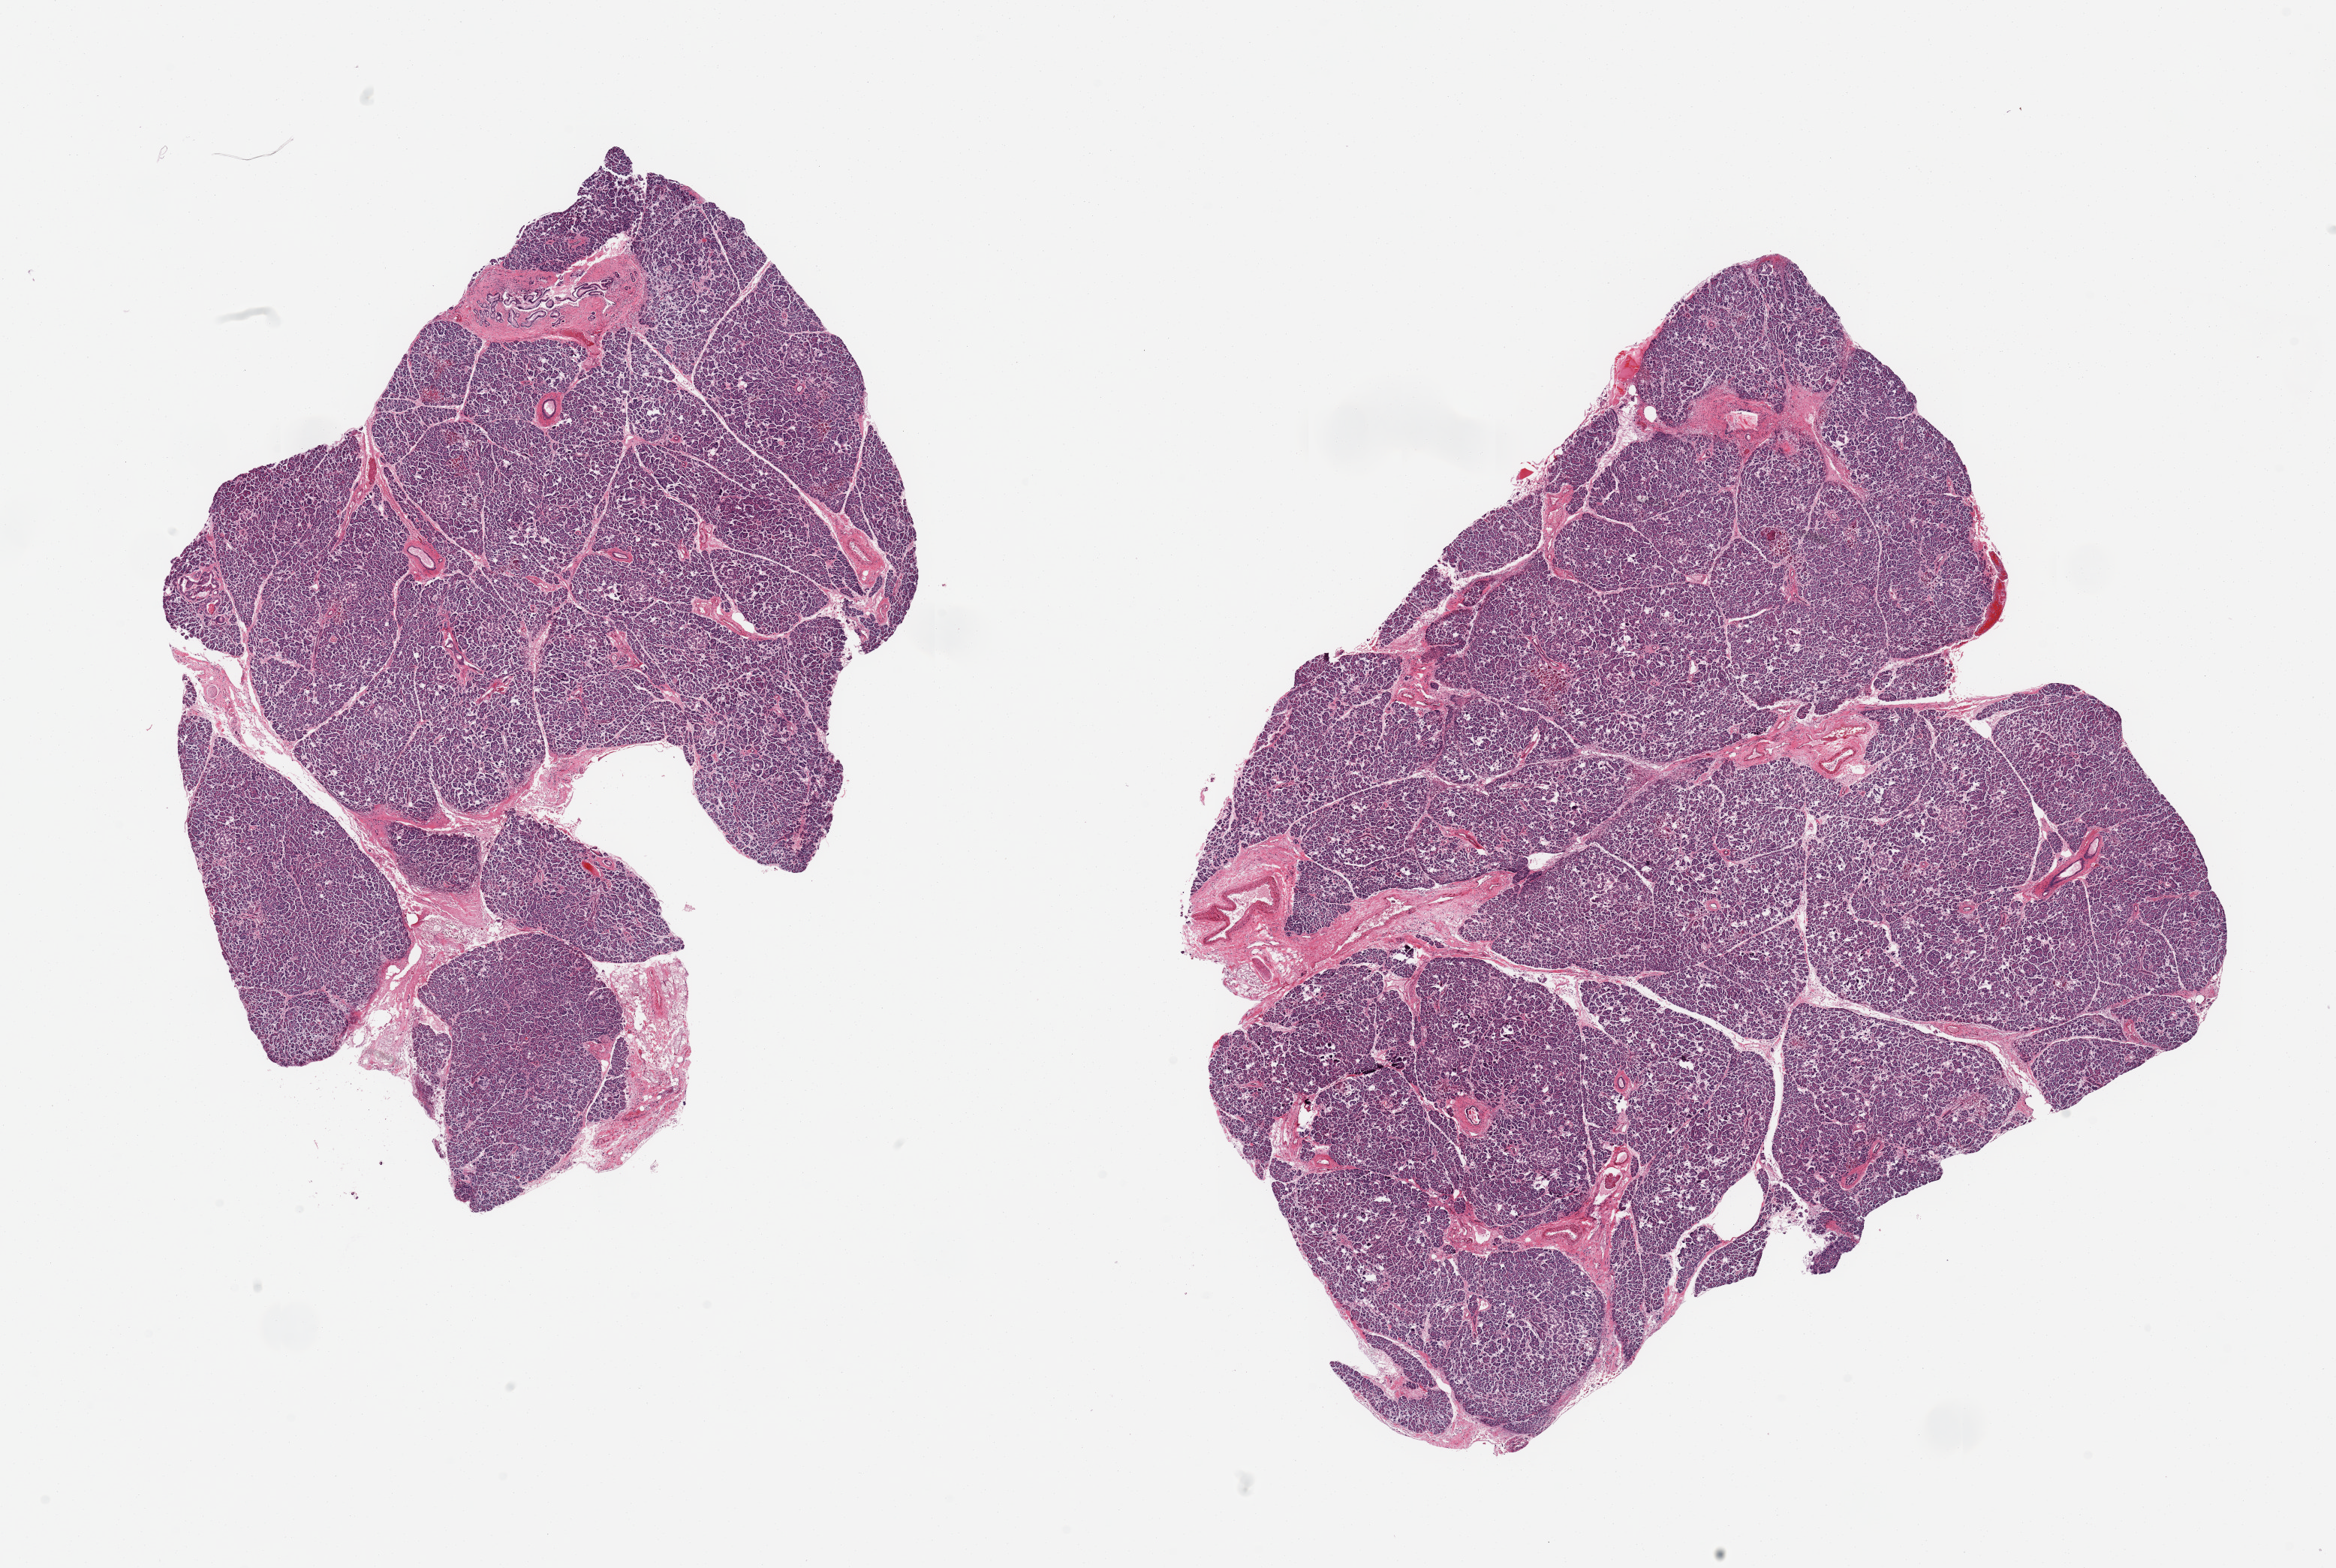
Whole-slide image, hematoxylin and eosin (H&E) stain, a low-resolution overview of the entire scanned area, about 24.6 x 16.5 mm, PAXgene-fixed paraffin-embedded (PFPE) section, sampled site (target tissue): pancreas, donor tissue sample. Donor: male.
Review note (as recorded): 2 pieces, moderately advanced saponification, Islets largely degenerated.